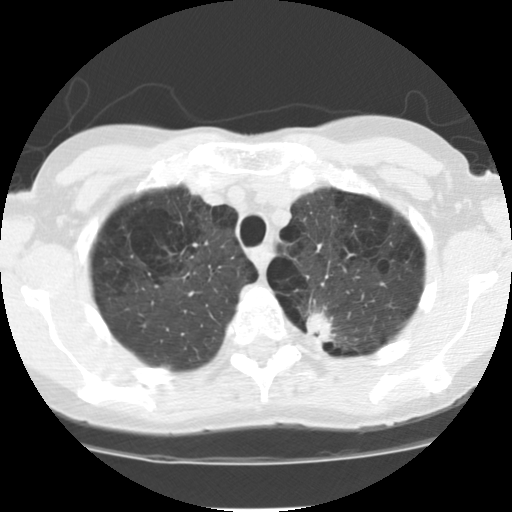
Low-dose screening chest CT, one axial slice. Slice 95 of 116 in the series (ordered by position). Reconstruction kernel STANDARD. 120 kVp. Lung window (W 1500 / L -600 HU). 2.5 mm slice thickness. 512 × 512 image matrix.
Annotated regions visible in this slice (manually delineated by an expert):
- lesion 1 (tumor, upper lobe of left lung): box from (x=306, y=307) to (x=336, y=344) px